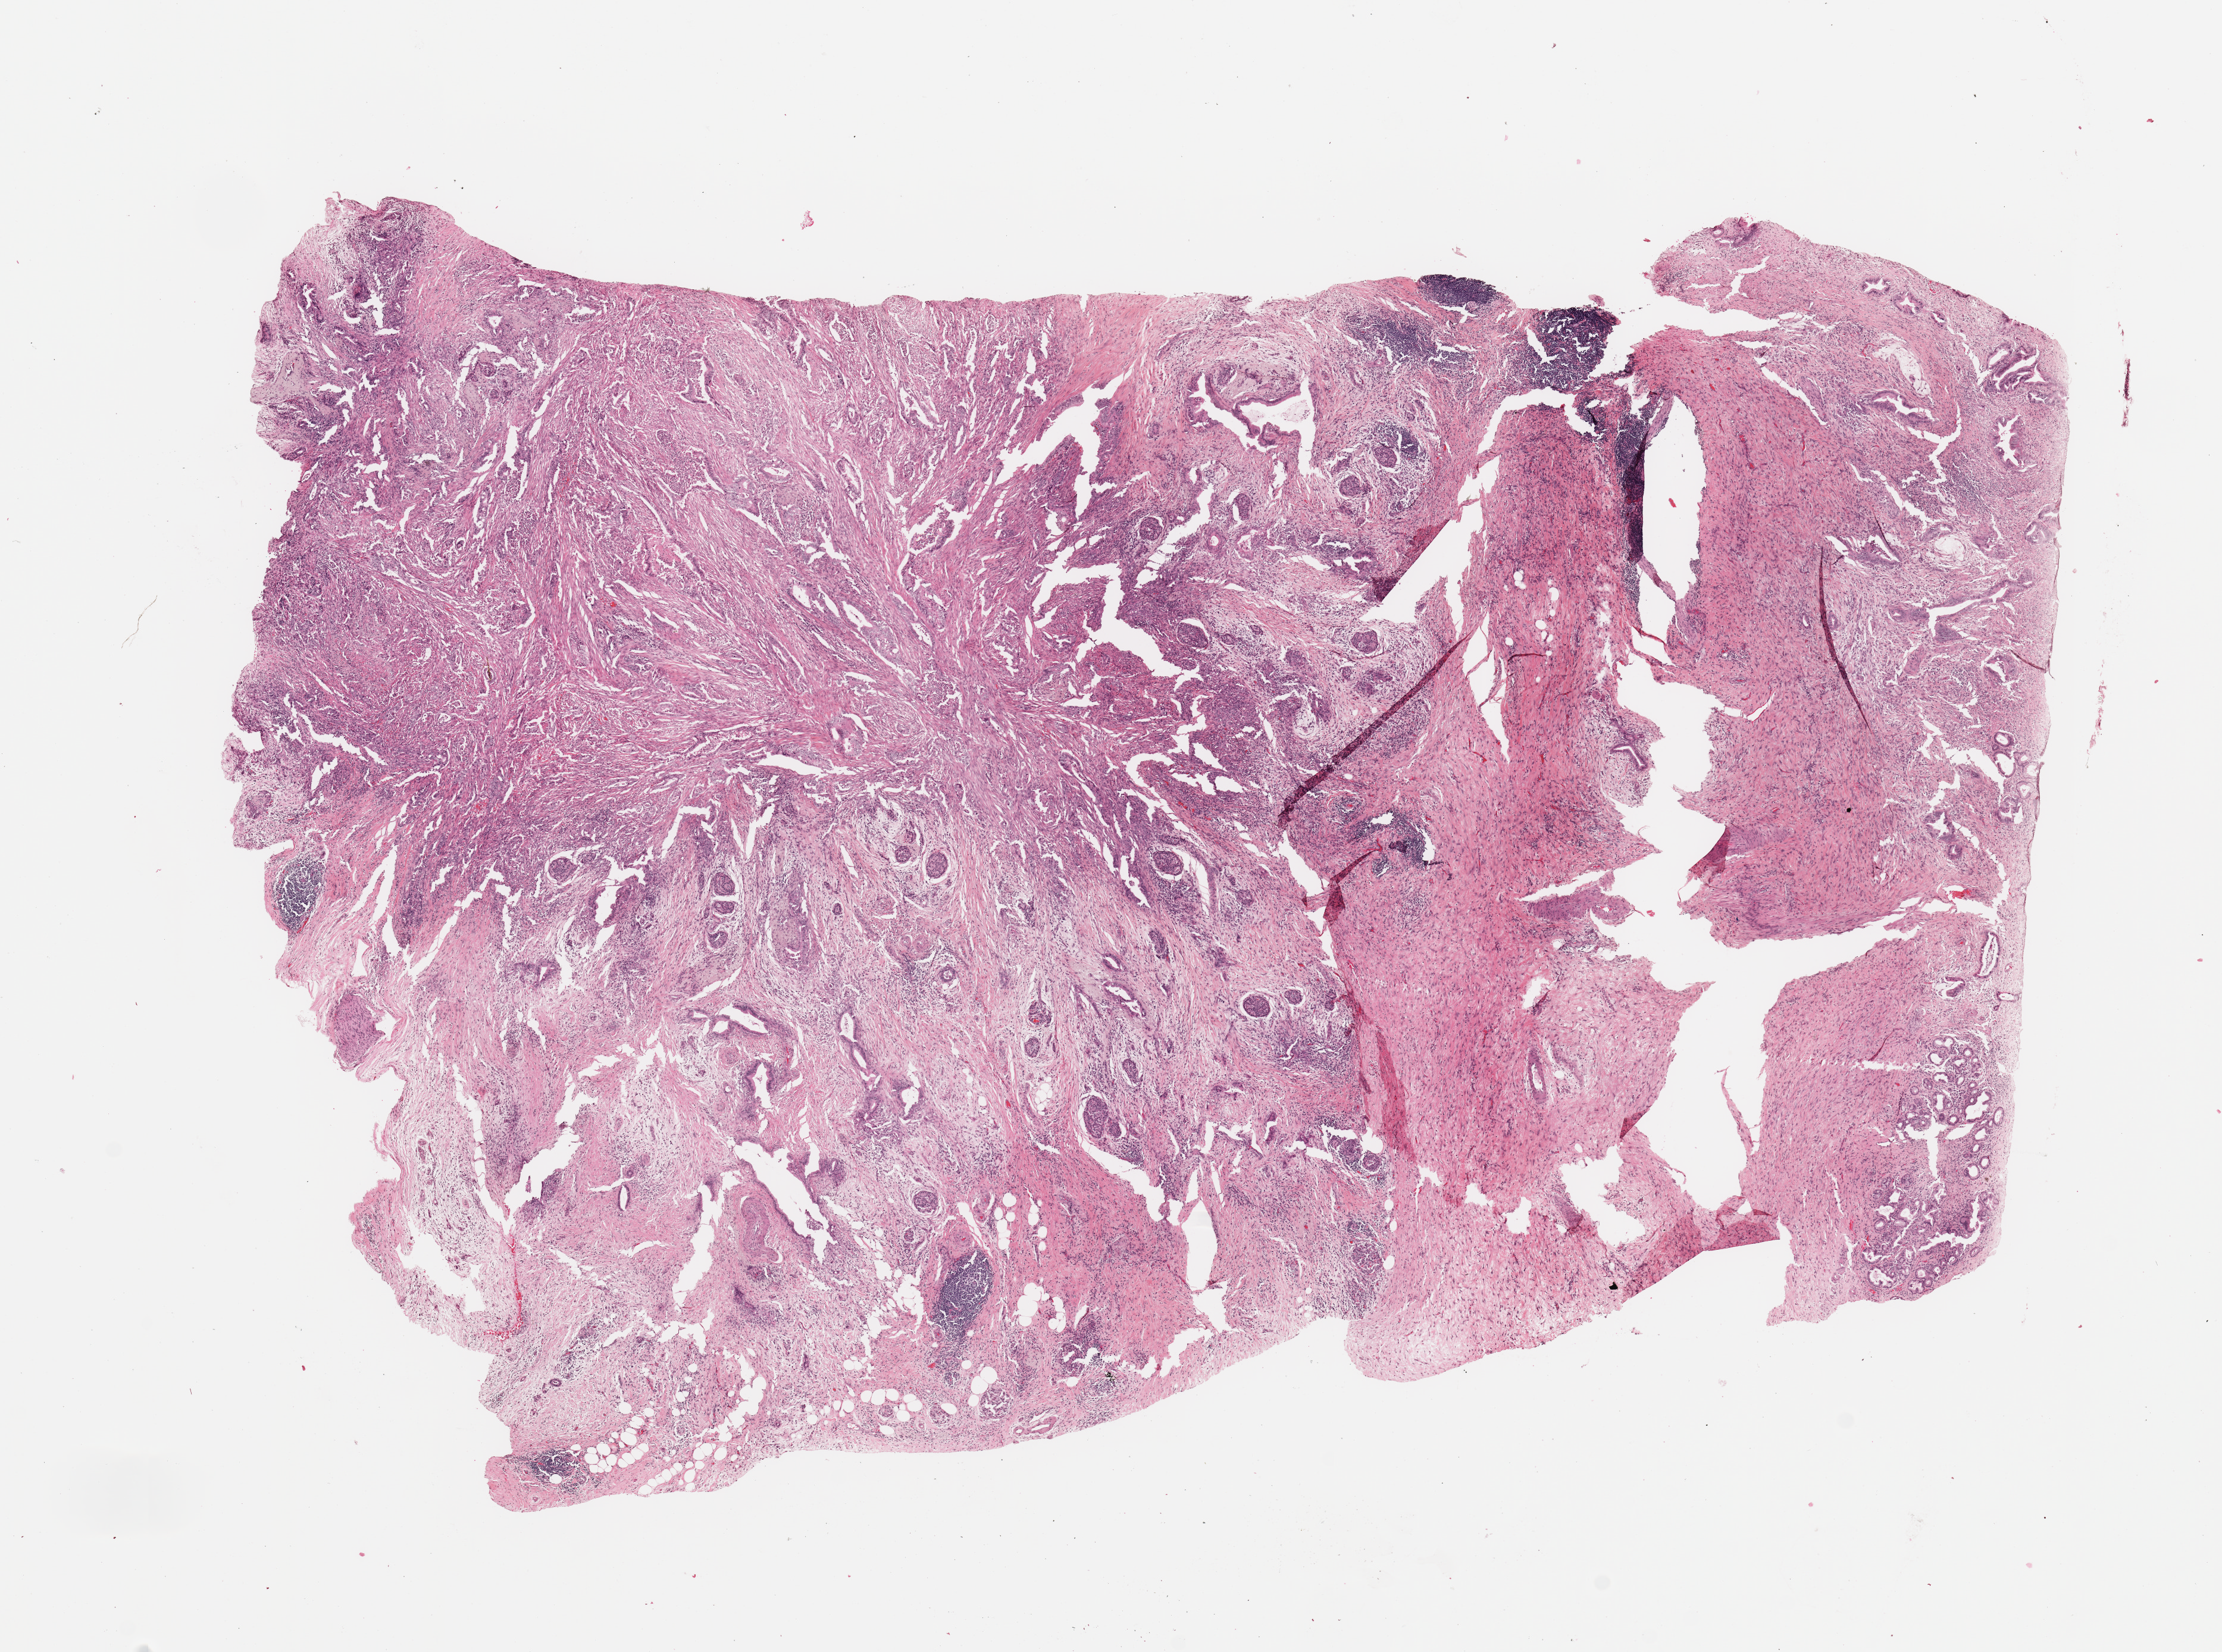
Whole-slide histology image, H&E-stained — shown as a low-resolution overview of the whole scanned area (about 14.8 x 11.0 mm, slide scanned at 20x); tumour tissue sample, sampled site: pancreas. Patient: female, age 70 years. Histologic grade: G2 (moderately differentiated). Pathologist review of this section (percent, as recorded): tumour nuclei 10%, necrosis 0%.
Primary tumour site (as recorded): head. AJCC pathologic stage: IIIB. Diagnosis: Infiltrating duct carcinoma, NOS.